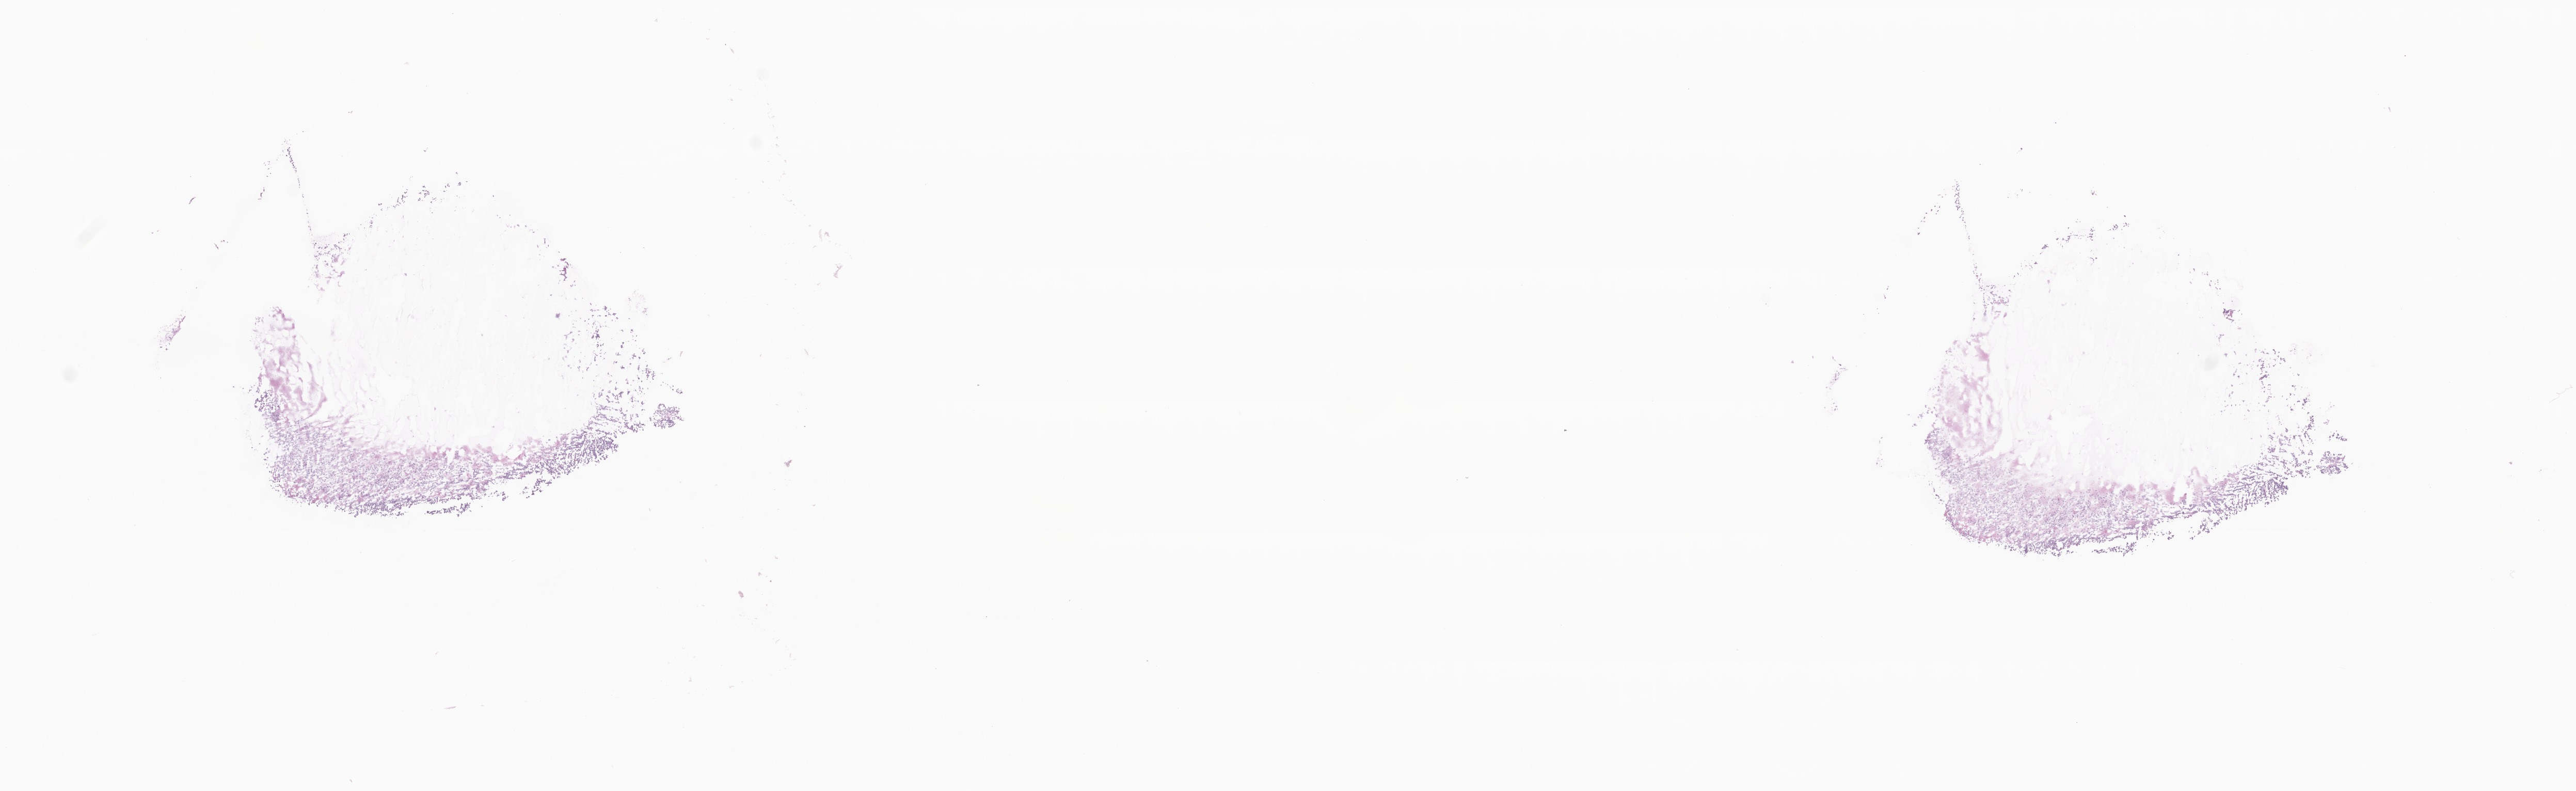
Whole-slide image, H&E stain, whole scanned area (about 21.0 x 6.5 mm) shown as a low-resolution overview. Frozen section (tissue freezing medium). Specimen: metastatic tumor tissue. Male, age 61 years at initial diagnosis. Slide review estimates, as recorded: tumor cells 80%, tumor nuclei 80%, stromal cells 20%, necrosis 0%, normal cells 0%. Infiltration values recorded for this section: lymphocyte infiltration 5%, monocyte infiltration 2%, neutrophil infiltration 8%.
• patient diagnosis (primary): Malignant melanoma, NOS
• section: top of the tissue portion